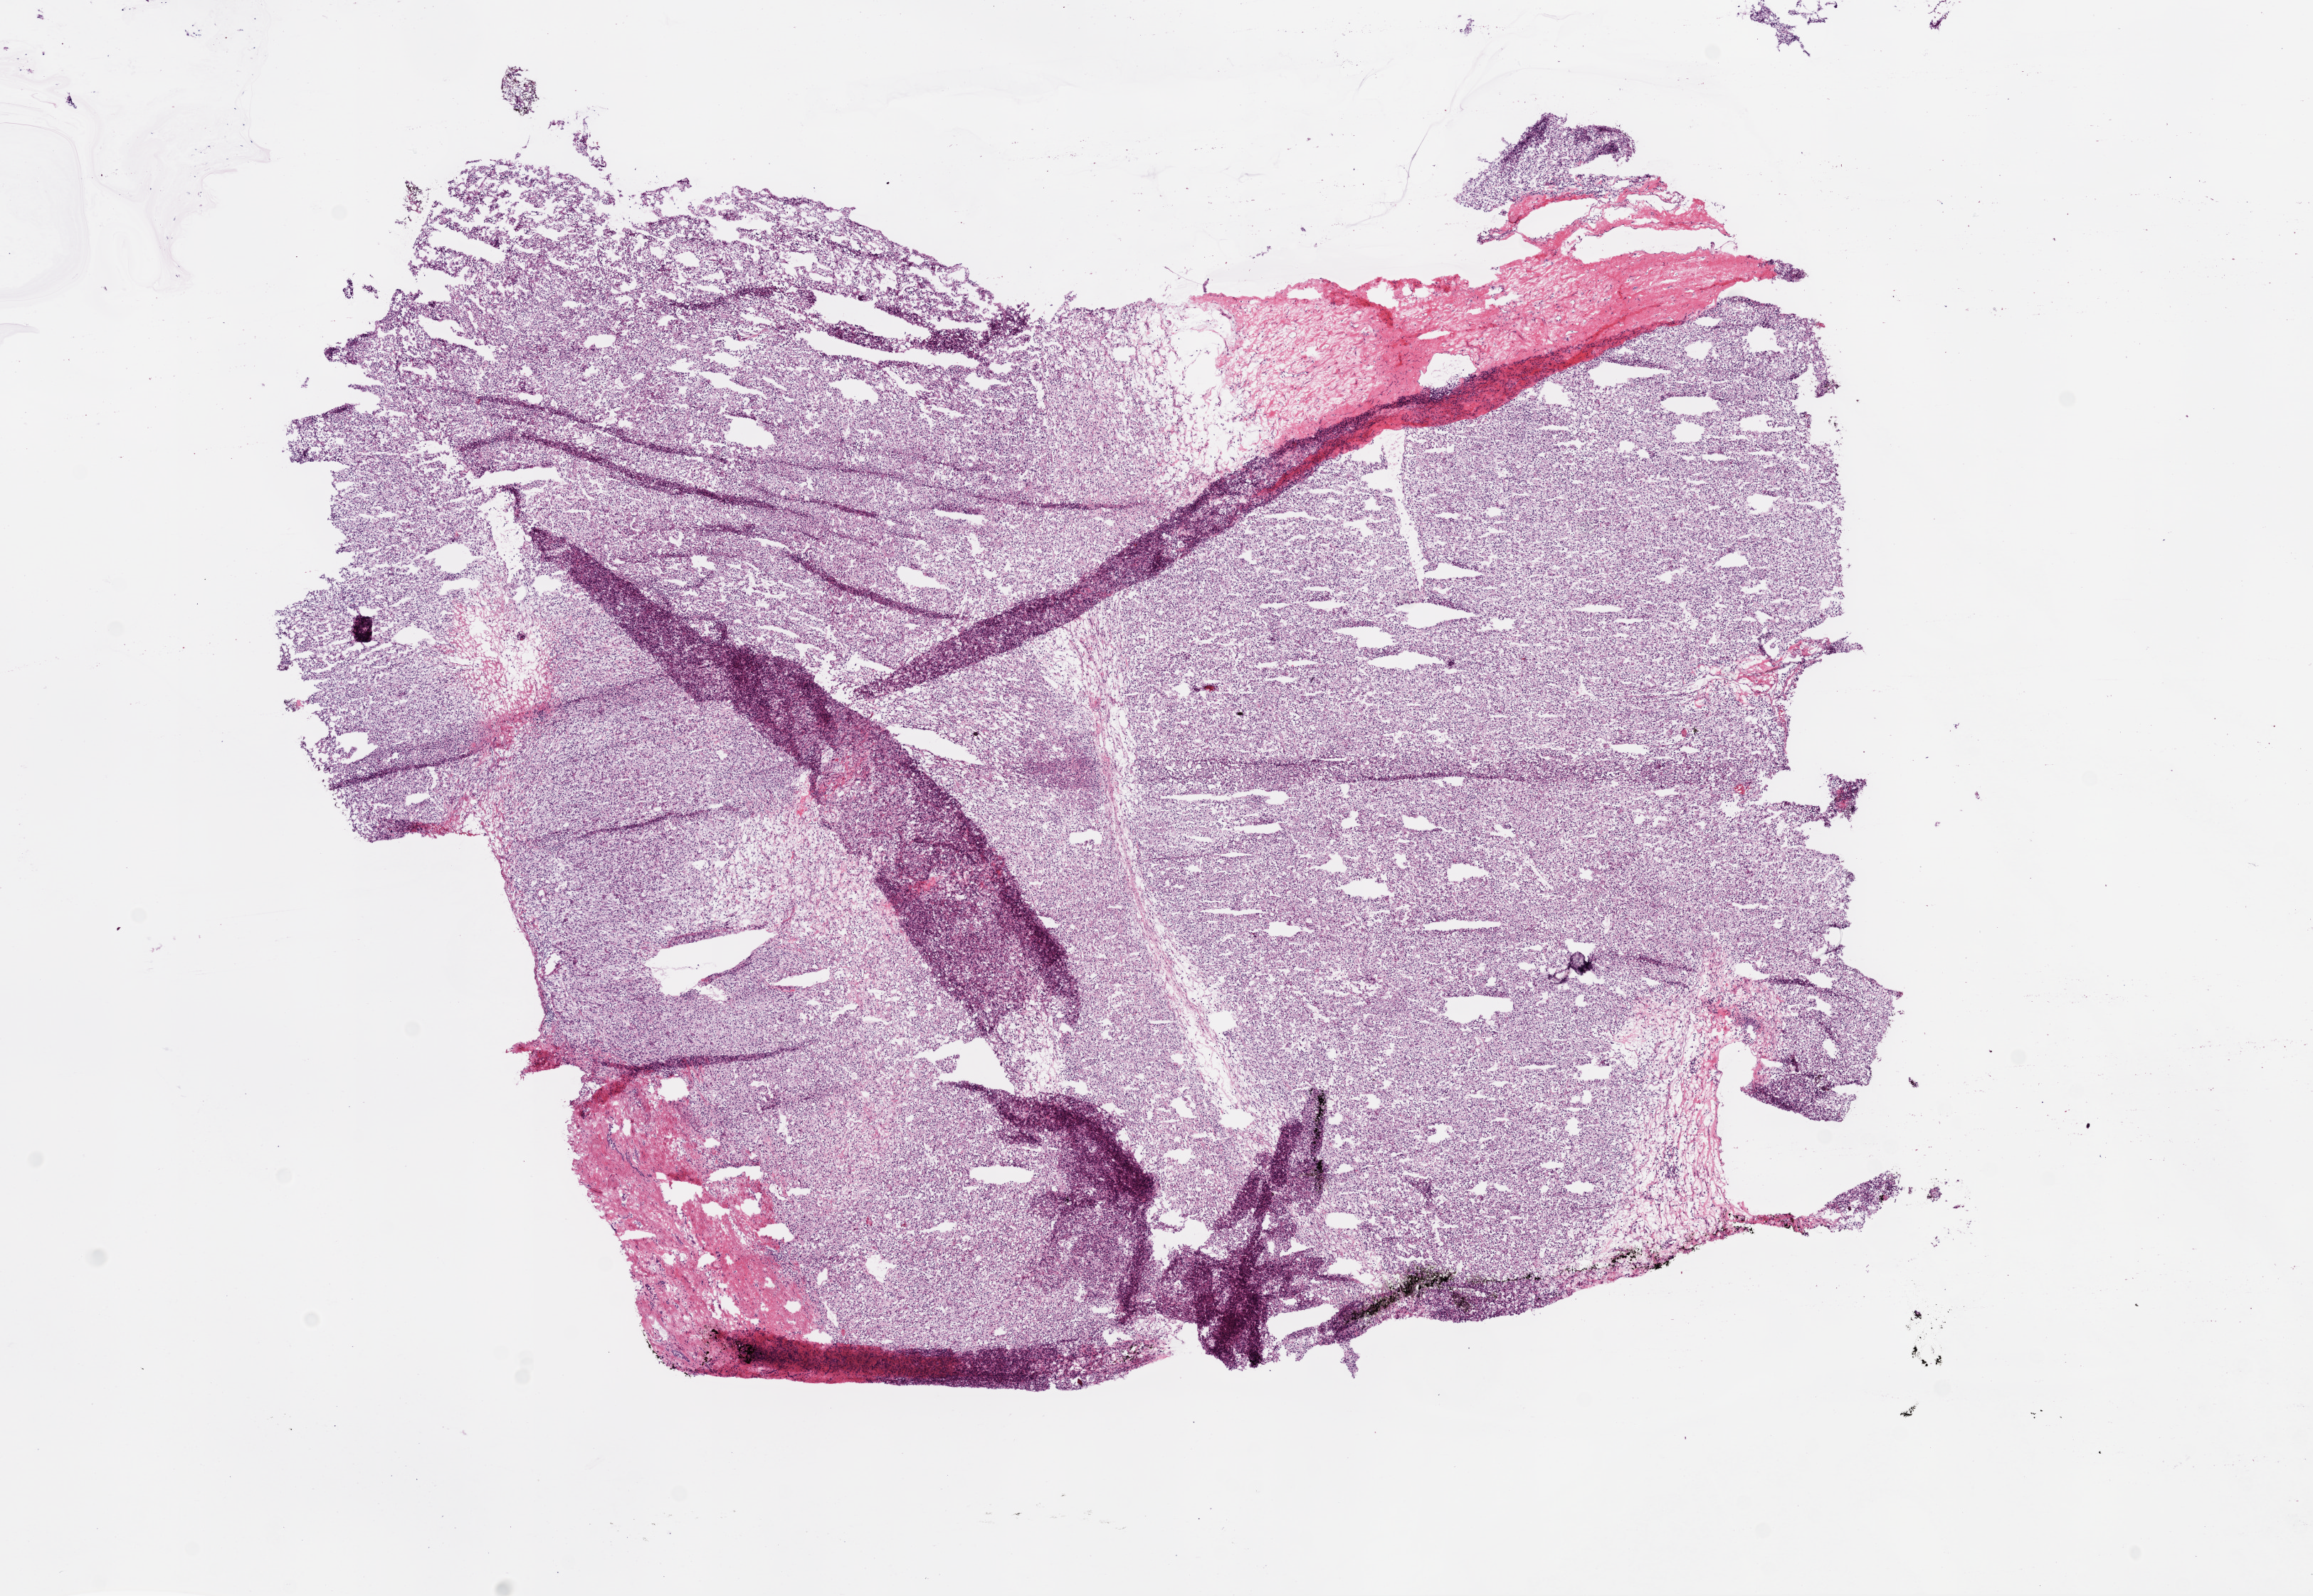
H&E whole-slide image, a low-resolution overview of the entire scanned area, about 13.0 x 9.0 mm (acquisition: 20x scan). Frozen section. Kidney, primary tumour sample. Patient: male, age at initial diagnosis 72 years. Composition of this section per pathologist review: tumour cells 85%, tumour nuclei 85%.
Pathologic diagnosis: Clear cell adenocarcinoma, NOS.